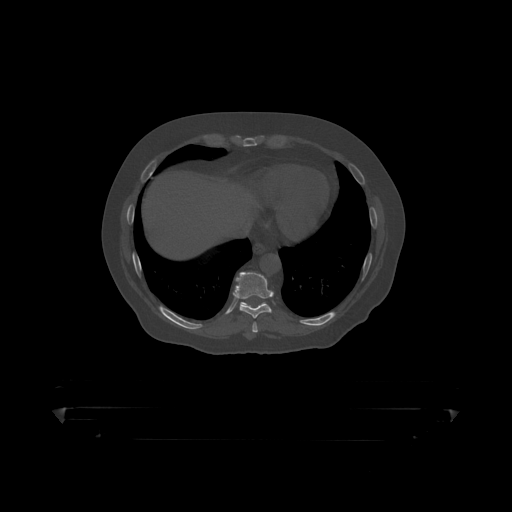
CT including the spine, one axial slice; slice 235 of 390 in the series (ordered by position); bone window (W 1800 / L 400 HU); 1.25 mm slice thickness; 512 × 512 image matrix. Patient: male, 60 years. From the clinical record (not read from this slice): primary cancer: prostate.
Outlined on this slice (semi-automatically segmented with operator editing):
- T10 vertebra: bounding box (x1, y1, x2, y2) in pixels: (241, 302, 246, 305)
- T9 vertebra: (234, 272, 274, 319)